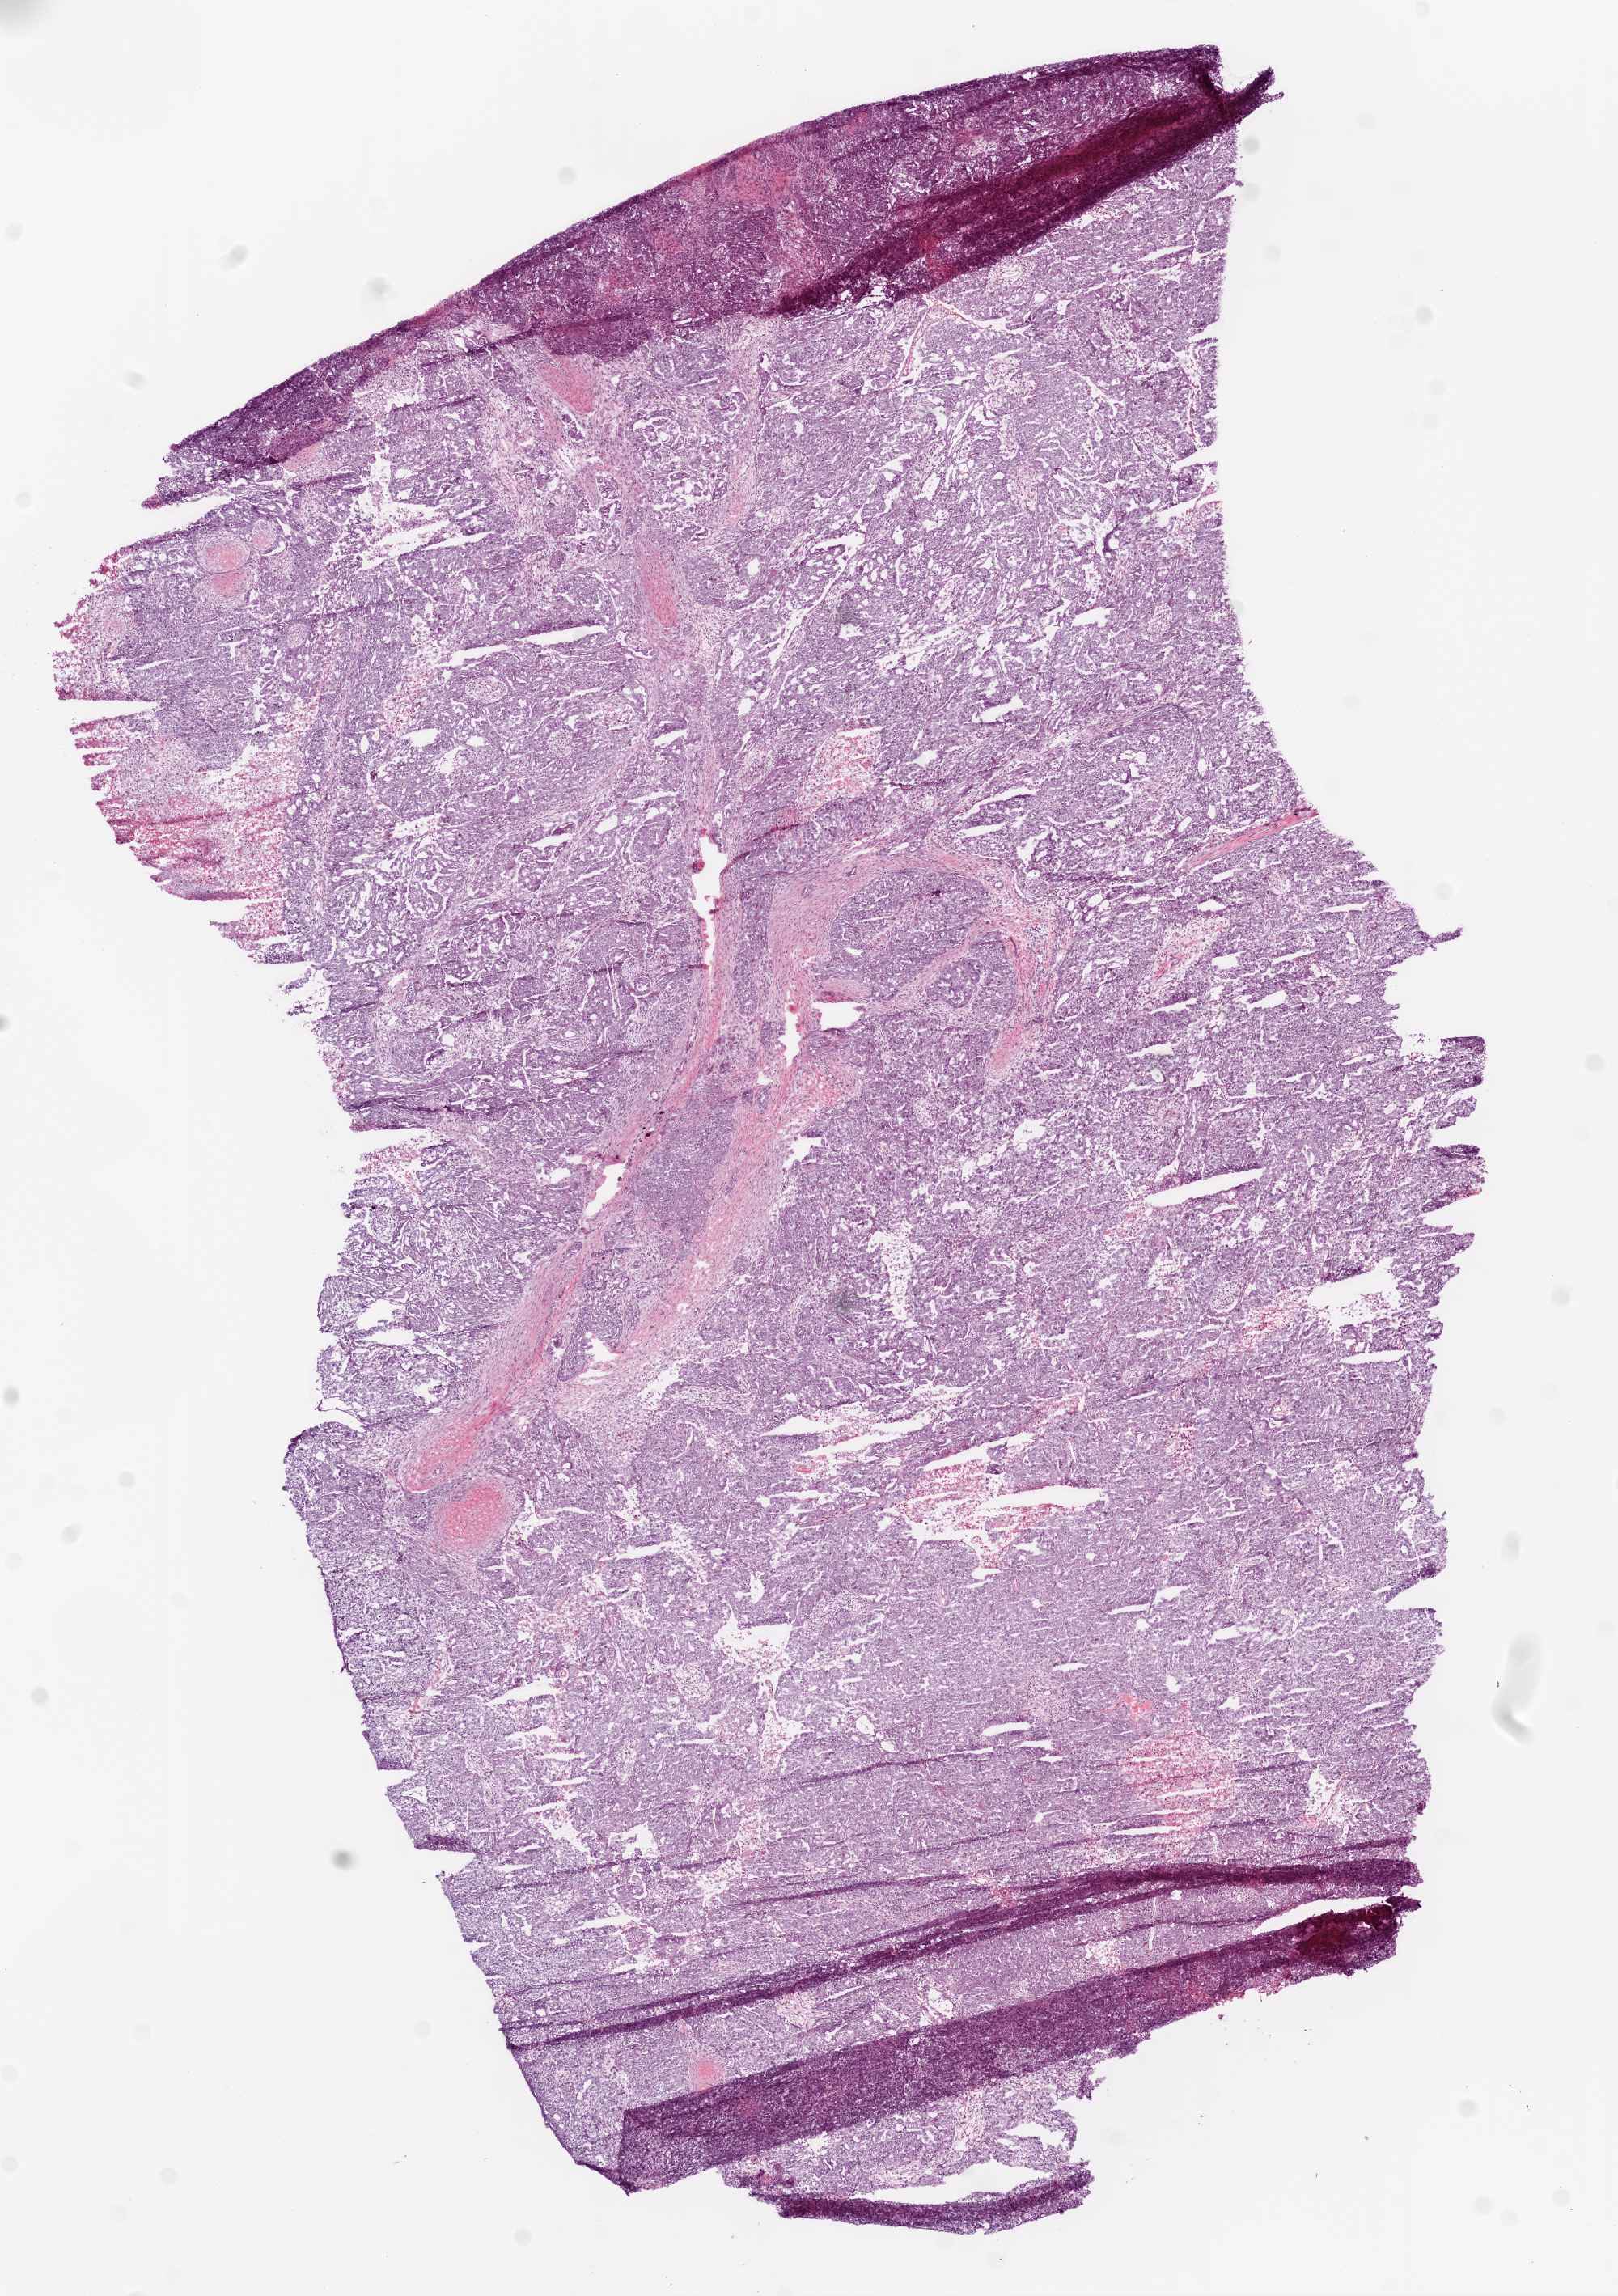
Whole-slide histology image, H&E, whole scanned area (about 8.0 x 11.4 mm) shown as a low-resolution overview, frozen section, sample: primary tumour, ovary. Female patient; age at initial diagnosis 80 years. Histologic grade: G3 (poorly differentiated). Pathologist review of this section (percent, as recorded): tumour cells 90%, tumour nuclei 95%, normal cells 0%, stromal cells 5%, necrosis 5%.
- pathologic diagnosis: Serous cystadenocarcinoma, NOS
- FIGO stage: IIIC
- laterality: bilateral